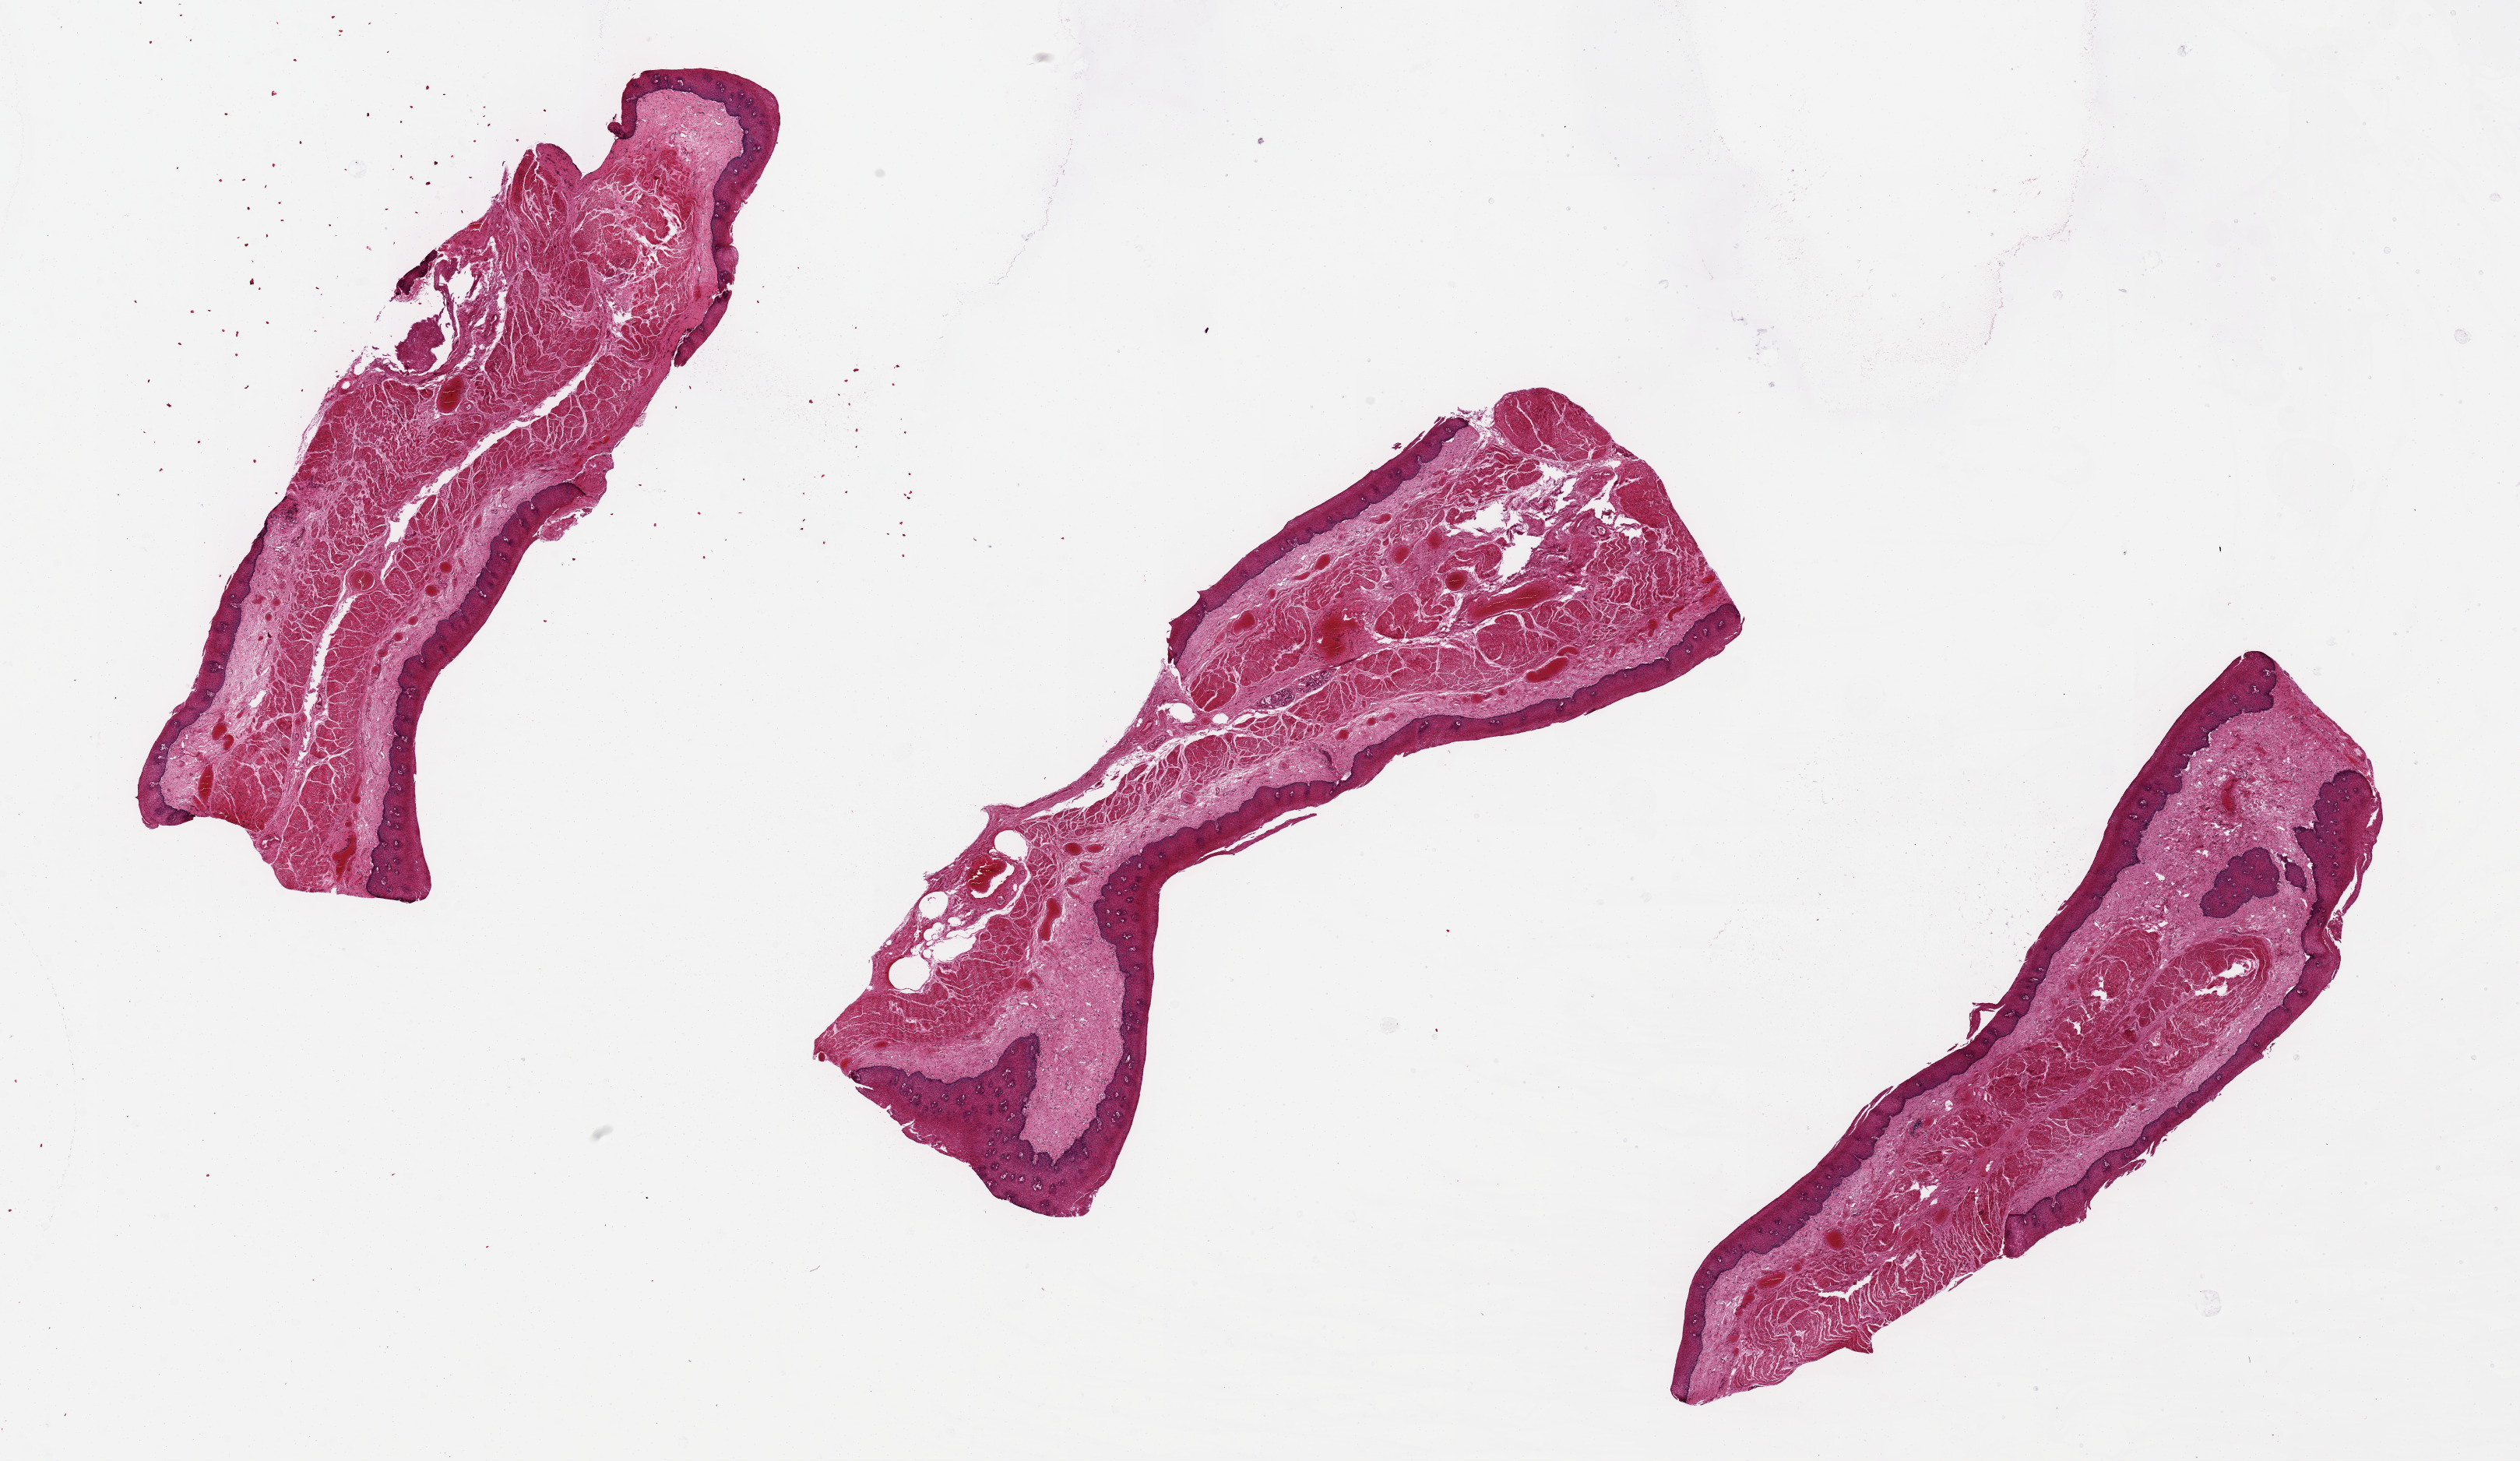
Whole-slide image, hematoxylin and eosin (H&E) stain, a low-resolution overview of the entire scanned area, about 25.6 x 14.8 mm (from a 20x scan). PAXgene-fixed, paraffin-embedded tissue. Target tissue: esophageal mucous membrane. Donor tissue sample. Male donor.
Review note (as recorded): Well preserved squamous layer. 9.5x1.7mm.